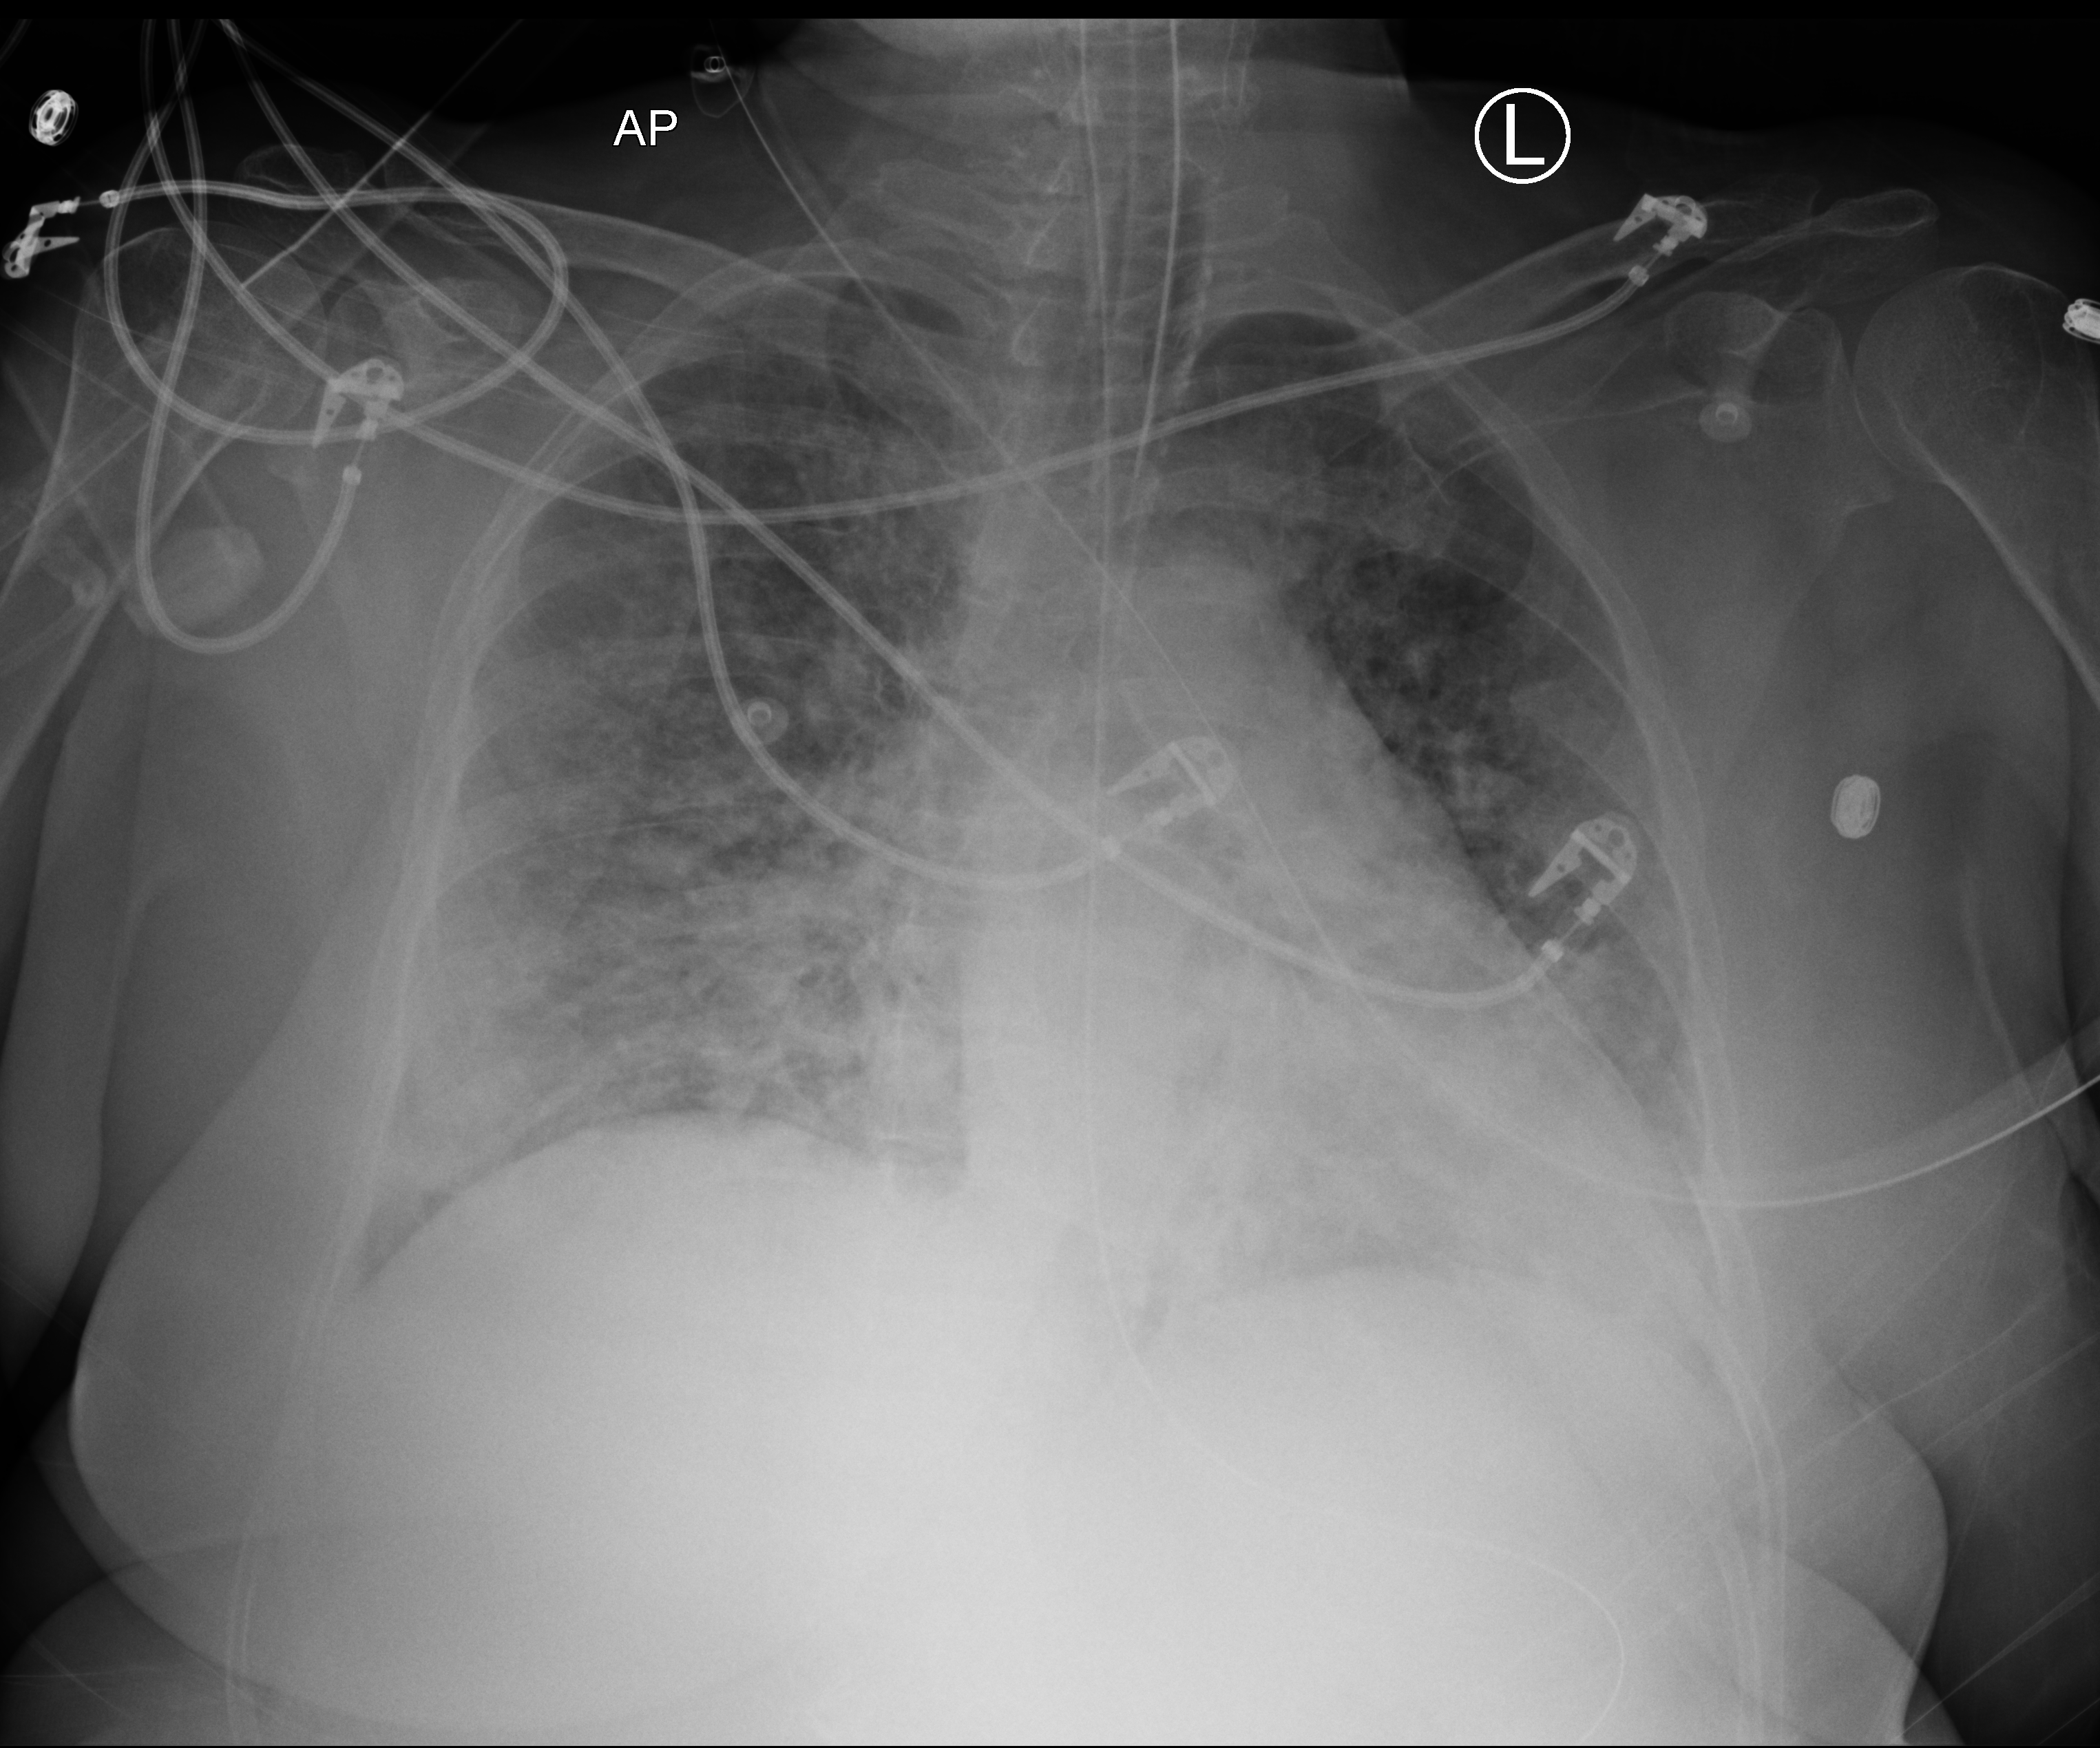
Bedside chest radiograph (computed radiography), anteroposterior (AP) projection. Patient hospitalised with COVID-19; female, aged 18–59 years.
Hospital-stay facts (about this admission, not read from this image; timing relative to this image not recorded): admitted to intensive care during this hospital stay: yes; hypertension (admission record): no.